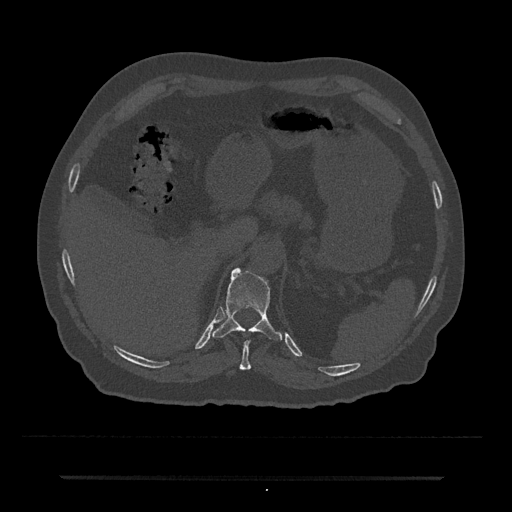
CT including the spine, one axial slice; position 189 of 797 along the scan axis; reconstruction kernel Br40s/3; 120 kVp; bone window (W 1800 / L 400 HU); 0.5 mm slice thickness; 512 × 512 image matrix. Male patient, age 69 years. Case-level facts recorded for this patient, not image findings: primary cancer: prostate.
Structures marked on this image (semi-automatically segmented with operator editing):
- T10 vertebra: bounding box [x1, y1, x2, y2] px = [240, 340, 251, 370]
- T11 vertebra: [212, 268, 283, 341]